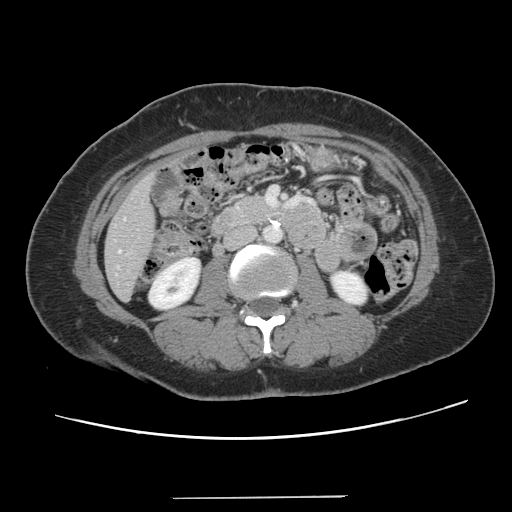
Contrast-enhanced abdominal CT, one axial slice; slice 36 of 141 in the series (ordered by position); intravenous contrast given; soft-tissue window (W 400 / L 40 HU); 2.5 mm slice thickness; 512 × 512 image matrix. Female patient, age 53 years. Case-level facts recorded for this patient, not image findings: diagnosis: colorectal cancer liver metastases, imaged before liver resection; multiple liver metastases: no; largest metastasis: 14.5 cm; disease in both lobes: yes.
Annotated regions visible in this slice (expert manual segmentation):
- liver: bounding box (x1, y1, x2, y2) in pixels: (105, 176, 156, 300)
- planned liver remnant (the part of the liver to remain after resection): (105, 212, 156, 299)